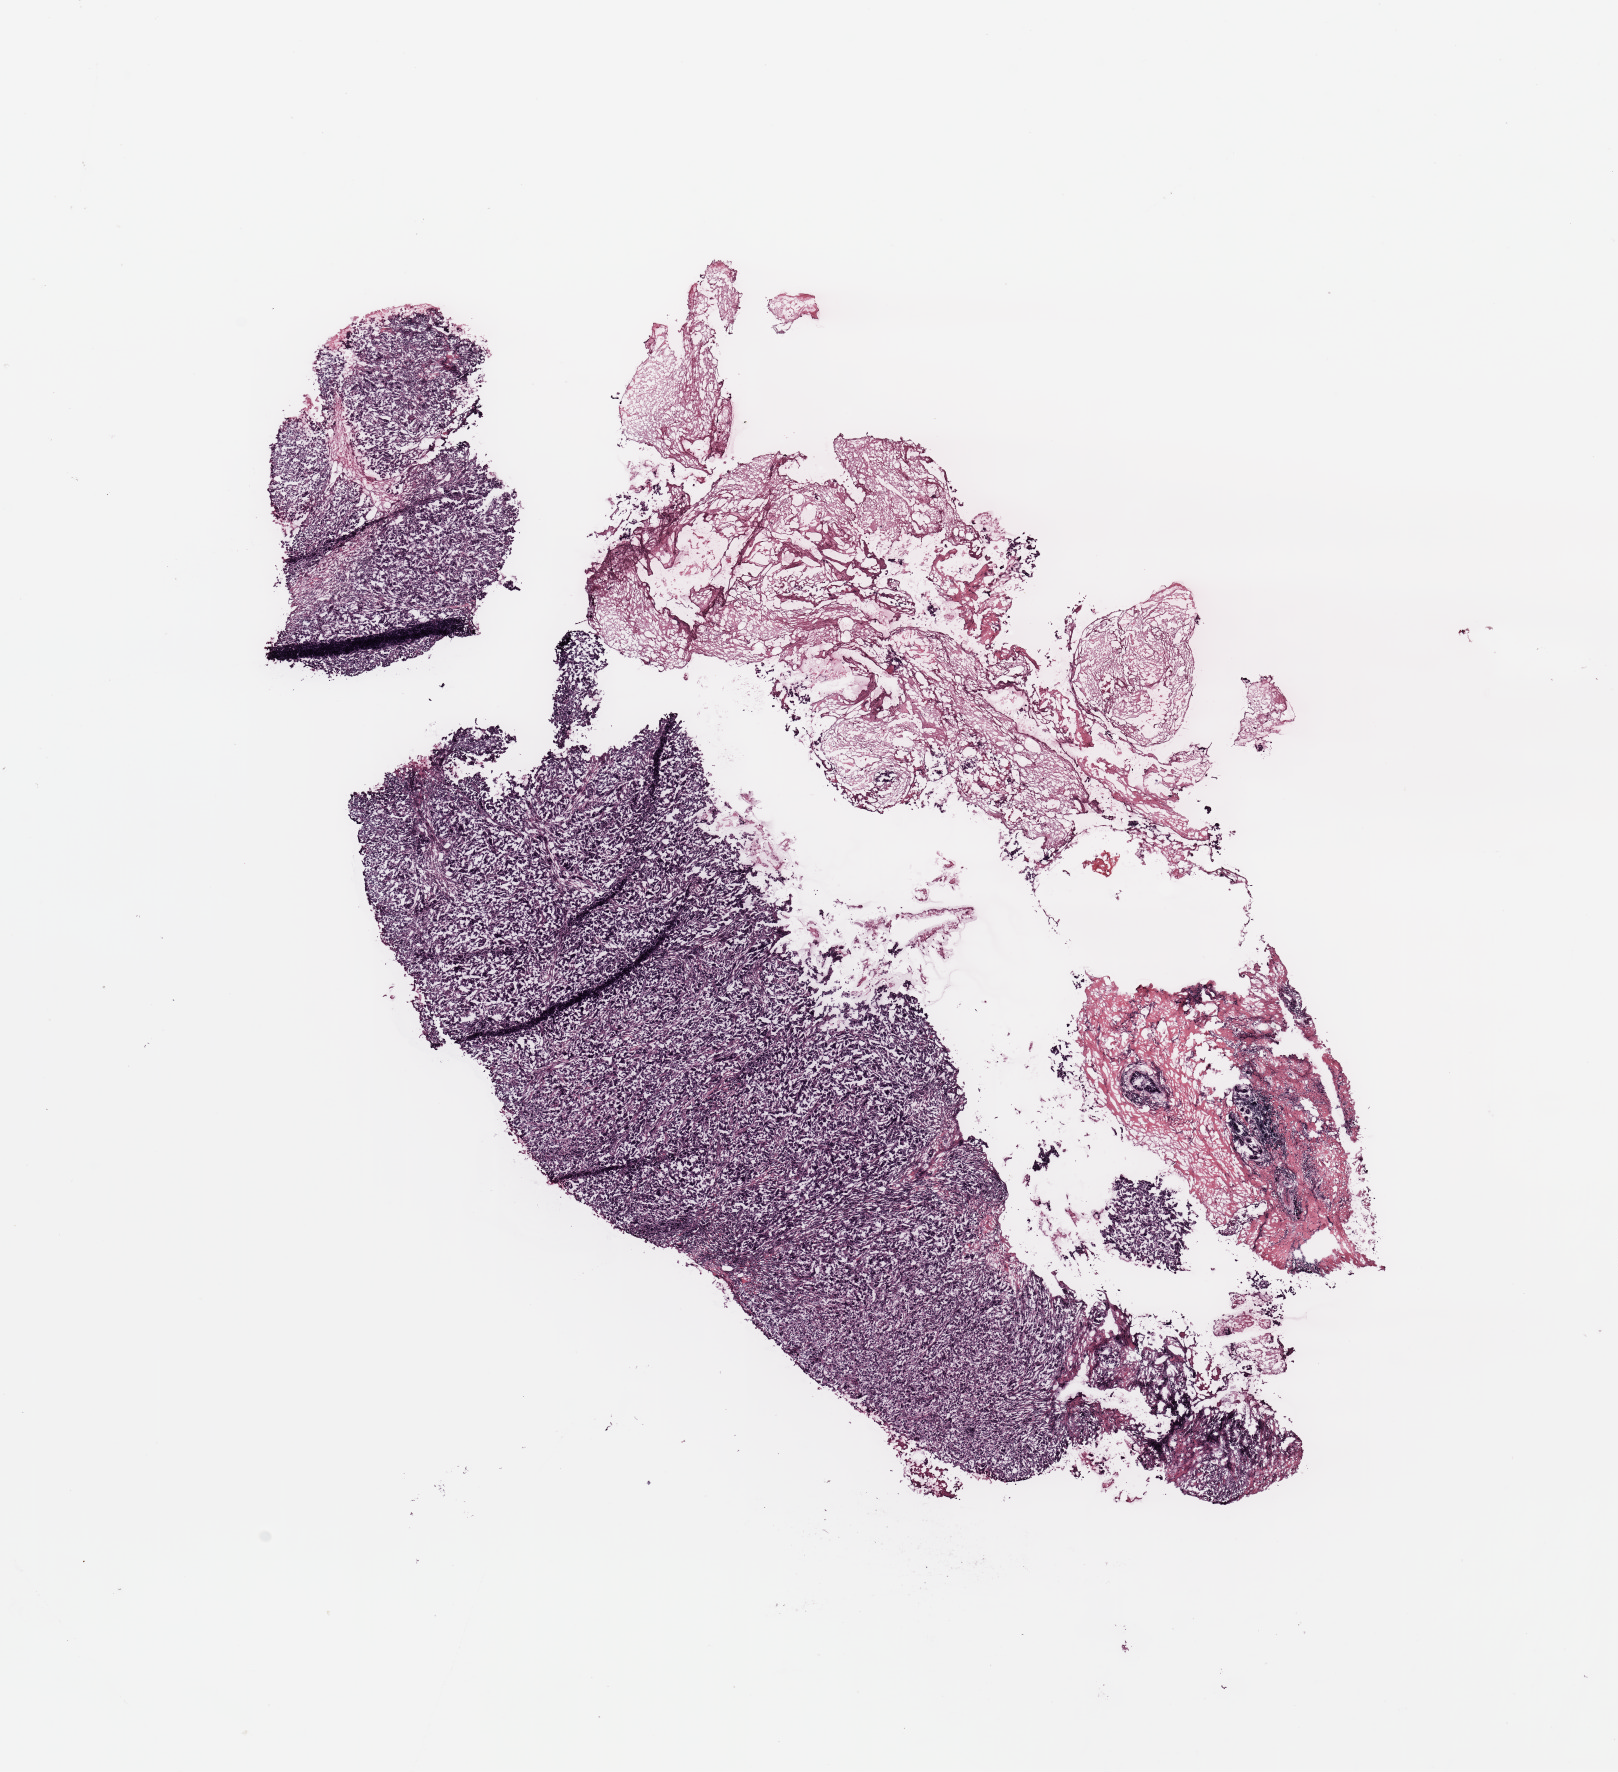
Hematoxylin and eosin (H&E) stained whole-slide image, shown as a low-resolution overview of the whole scanned area (about 12.8 x 14.0 mm, slide scanned at 20x); tumour tissue sample, breast. Female, 58 y/o.
- histologic diagnosis: Infiltrating duct carcinoma, NOS
- AJCC pathologic stage: II